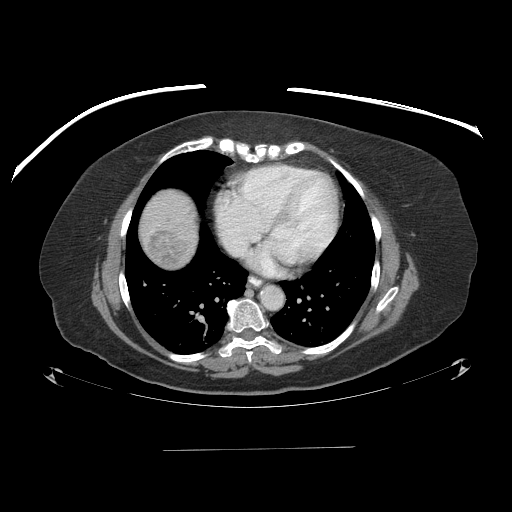
Contrast-enhanced abdominal CT (liver protocol), one axial slice; position 86 of 103 along the scan axis; reconstruction kernel STANDARD; 120 kVp; one of 2 acquisitions stored at this slice position; soft-tissue window (W 400 / L 40 HU); 2.5 mm slice thickness; 512 × 512 image matrix. From the clinical record (not read from this slice): diagnosis: hepatocellular carcinoma (patient treated with transarterial chemoembolisation; whether this scan precedes or follows treatment is not stated here); TNM stage (as recorded): Stage-IIIA; Child-Pugh class: A; tumour nodularity: multinodular.
Structures marked on this image (semi-automatic segmentation, software-assisted and operator-edited):
- liver parenchyma outside the tumour (the mass and vessels are separate outlines, so this box may not span the whole liver): box from (x=140, y=188) to (x=196, y=266) px
- mass: (x=148, y=230)–(x=186, y=264)